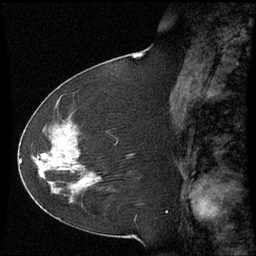
Breast MRI (dynamic contrast-enhanced), one sagittal slice; dynamic contrast-enhanced series, image 2 of 3 at this slice position (ordered by acquisition); 1.5 T; TE 4.2 ms, TR 8.9 ms; 2.3 mm slice thickness; 256 × 256 image matrix, field of view 210 × 210 mm. Female patient, age 51 years. From the clinical record (not read from this slice): setting: breast cancer imaged before/during neoadjuvant chemotherapy; receptor status: HR-positive, HER2-negative.
Annotated regions visible in this slice (semi-automatic segmentation, software-assisted and operator-edited):
- analysis volume of interest (the breast-tissue region the enhancement analysis was run in; not a lesion): bounding box [x1, y1, x2, y2] px = [50, 118, 102, 187]
- tumour enhancement mask (voxels above the 70 % enhancement threshold inside the analysis volume of interest): [50, 130, 85, 182]